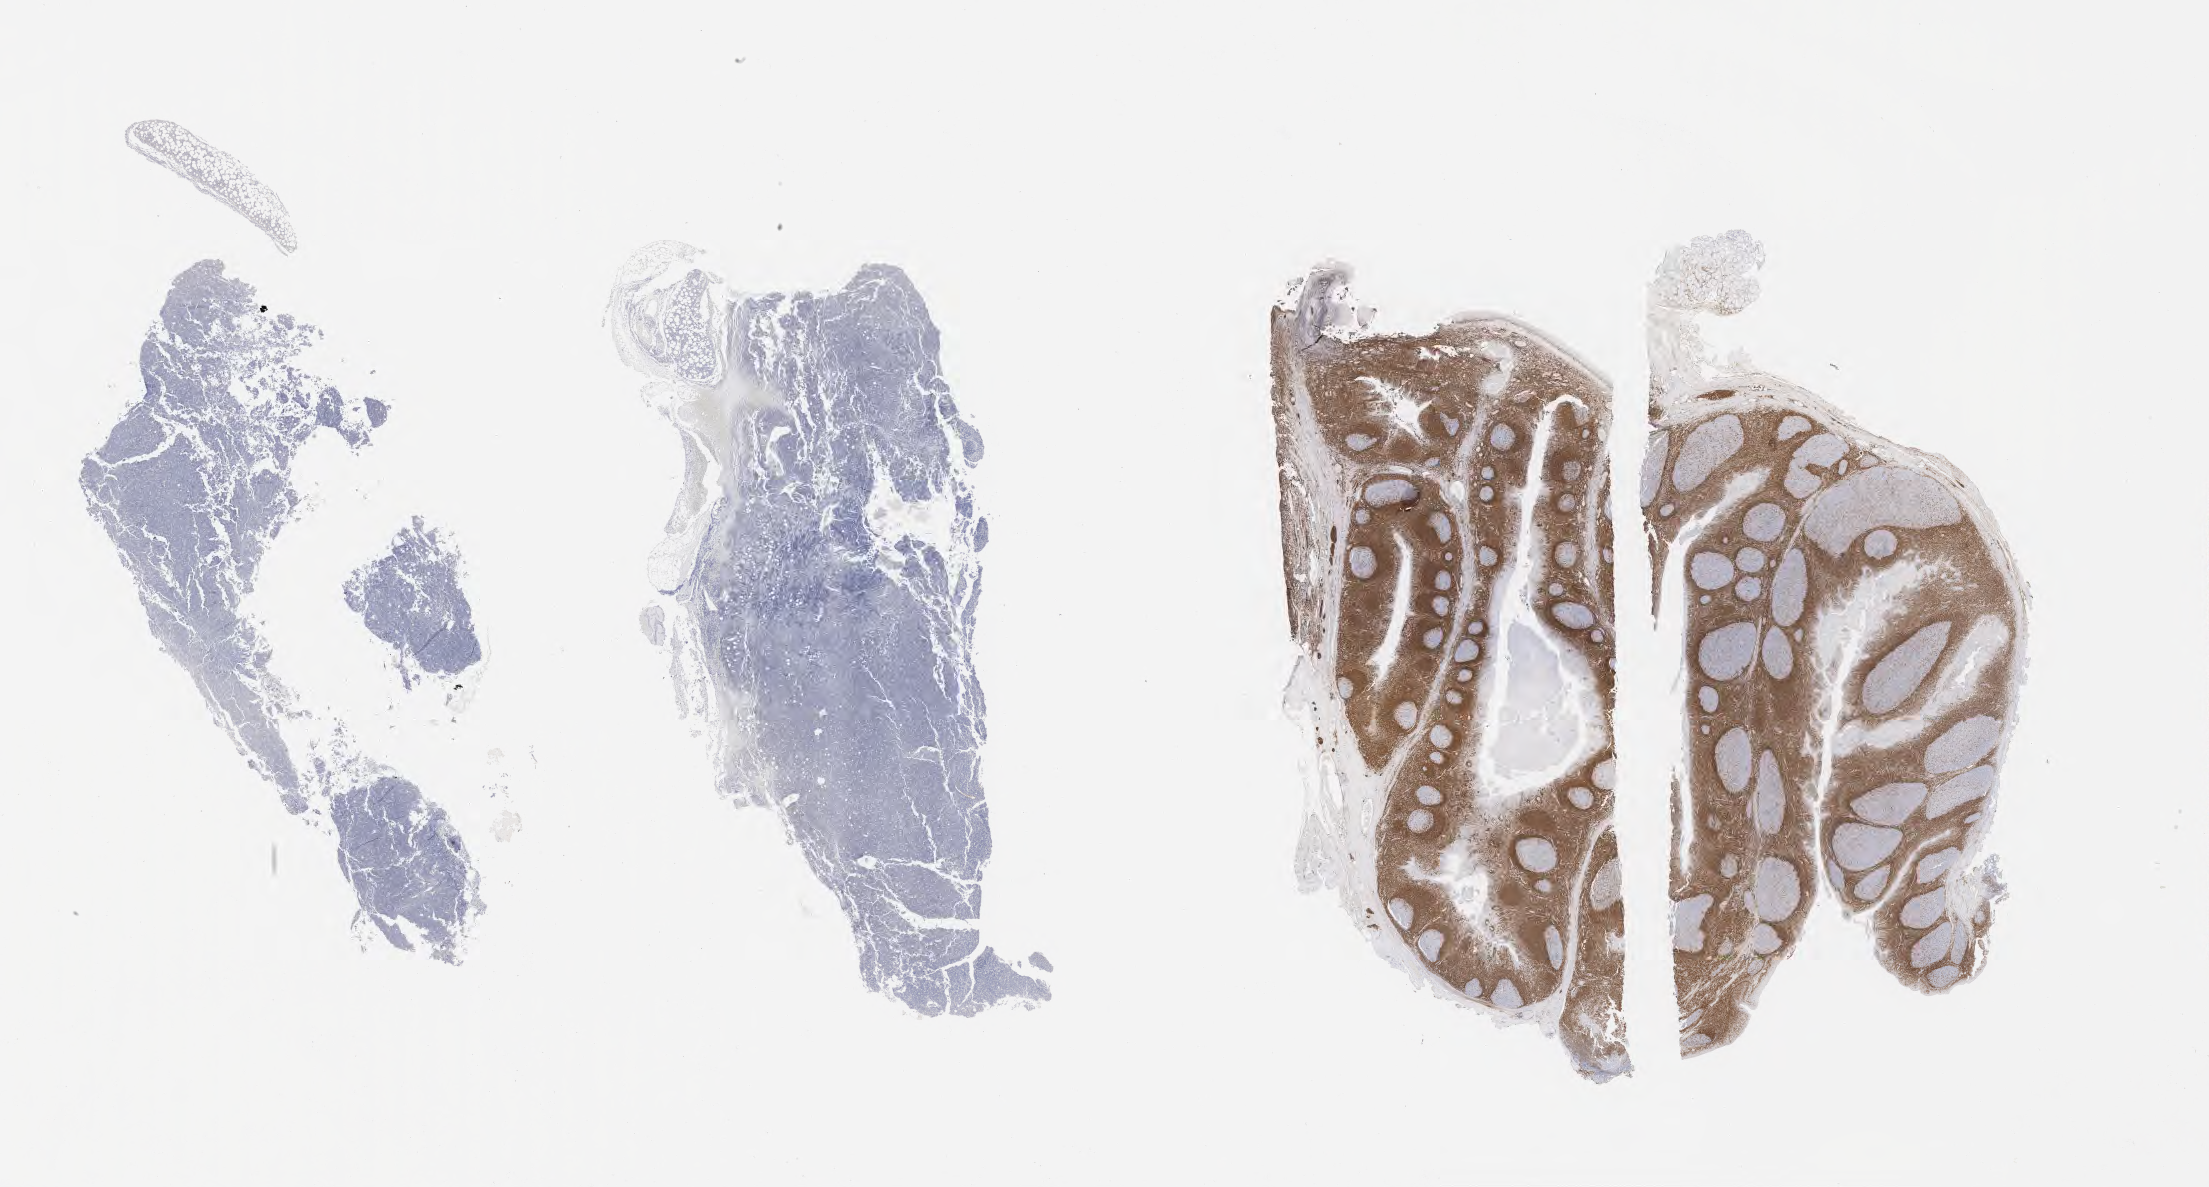
Whole-slide image, immunohistochemical stain for BCL2 — whole scanned area (about 35.7 x 19.2 mm) shown as a low-resolution overview, specimen: tumor tissue. Patient: female, age 16 years.
• diagnosis: Burkitt lymphoma, NOS